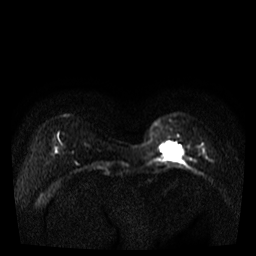
Breast MRI, one axial slice. Slice 9 of 35 in the series (ordered by position). Diffusion-weighted series; image 2 of 4 stored at this slice position (different b-values; order by instance number). 3 T. 5 mm slice thickness. 256 × 256 image matrix. Female patient.
Annotated regions visible in this slice (expert manual segmentation):
- tumour on diffusion-weighted imaging: bounding box (x1, y1, x2, y2) in pixels: (167, 145, 182, 158)